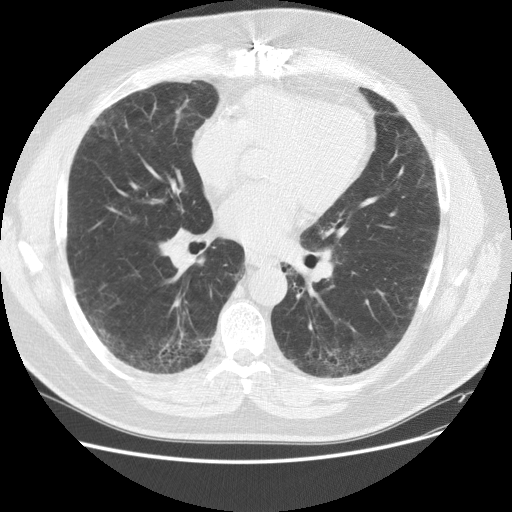
Axial slice from a low-dose chest CT screening exam; baseline screening round; lung window (W 1500 / L -600 HU); standard (soft-tissue) reconstruction kernel (STANDARD); 120 kVp; slice 72 of 151 in the series. Male participant, aged 59 years at enrolment.
Expert reader's lesion annotation, bounding box (x1, y1, x2, y2) in pixels: (81, 99, 133, 149). The screening reader recorded 2 non-calcified nodules or masses ≥4 mm on this exam (right middle lobe, right lower lobe); which of them this box marks is not recorded. Official screen result: positive, change unspecified: nodule(s) >= 4 mm or enlarging nodule(s), mass(es), or other non-specific abnormalities suspicious for lung cancer.